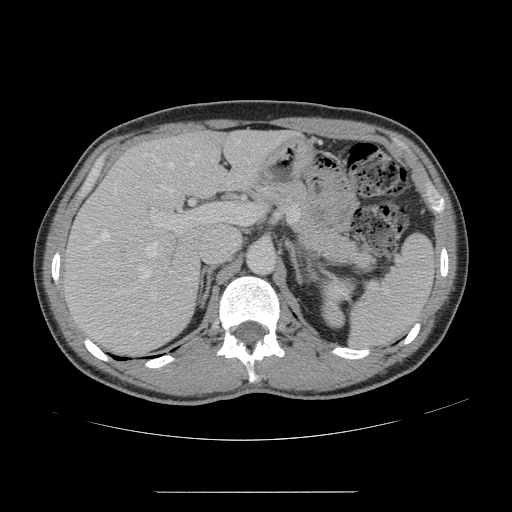
Contrast-enhanced abdominal CT, one axial slice; position 92 of 178 along the scan axis; 120 kVp; intravenous contrast given; soft-tissue window (W 400 / L 40 HU); 2.5 mm slice thickness; 512 × 512 image matrix, field of view 401 × 401 mm. Male patient, age 53 years. From the clinical record (not read from this slice): diagnosis: colorectal cancer liver metastases, imaged before liver resection; multiple liver metastases: yes; largest metastasis: 2.4 cm.
Outlined on this slice (outlined manually by an expert reader):
- hepatic veins: bounding box (x1, y1, x2, y2) in pixels: (95, 162, 193, 281)
- liver: (67, 131, 286, 353)
- planned liver remnant (the part of the liver to remain after resection): (149, 130, 284, 193)
- portal vein (with intrahepatic branches): (151, 203, 257, 281)